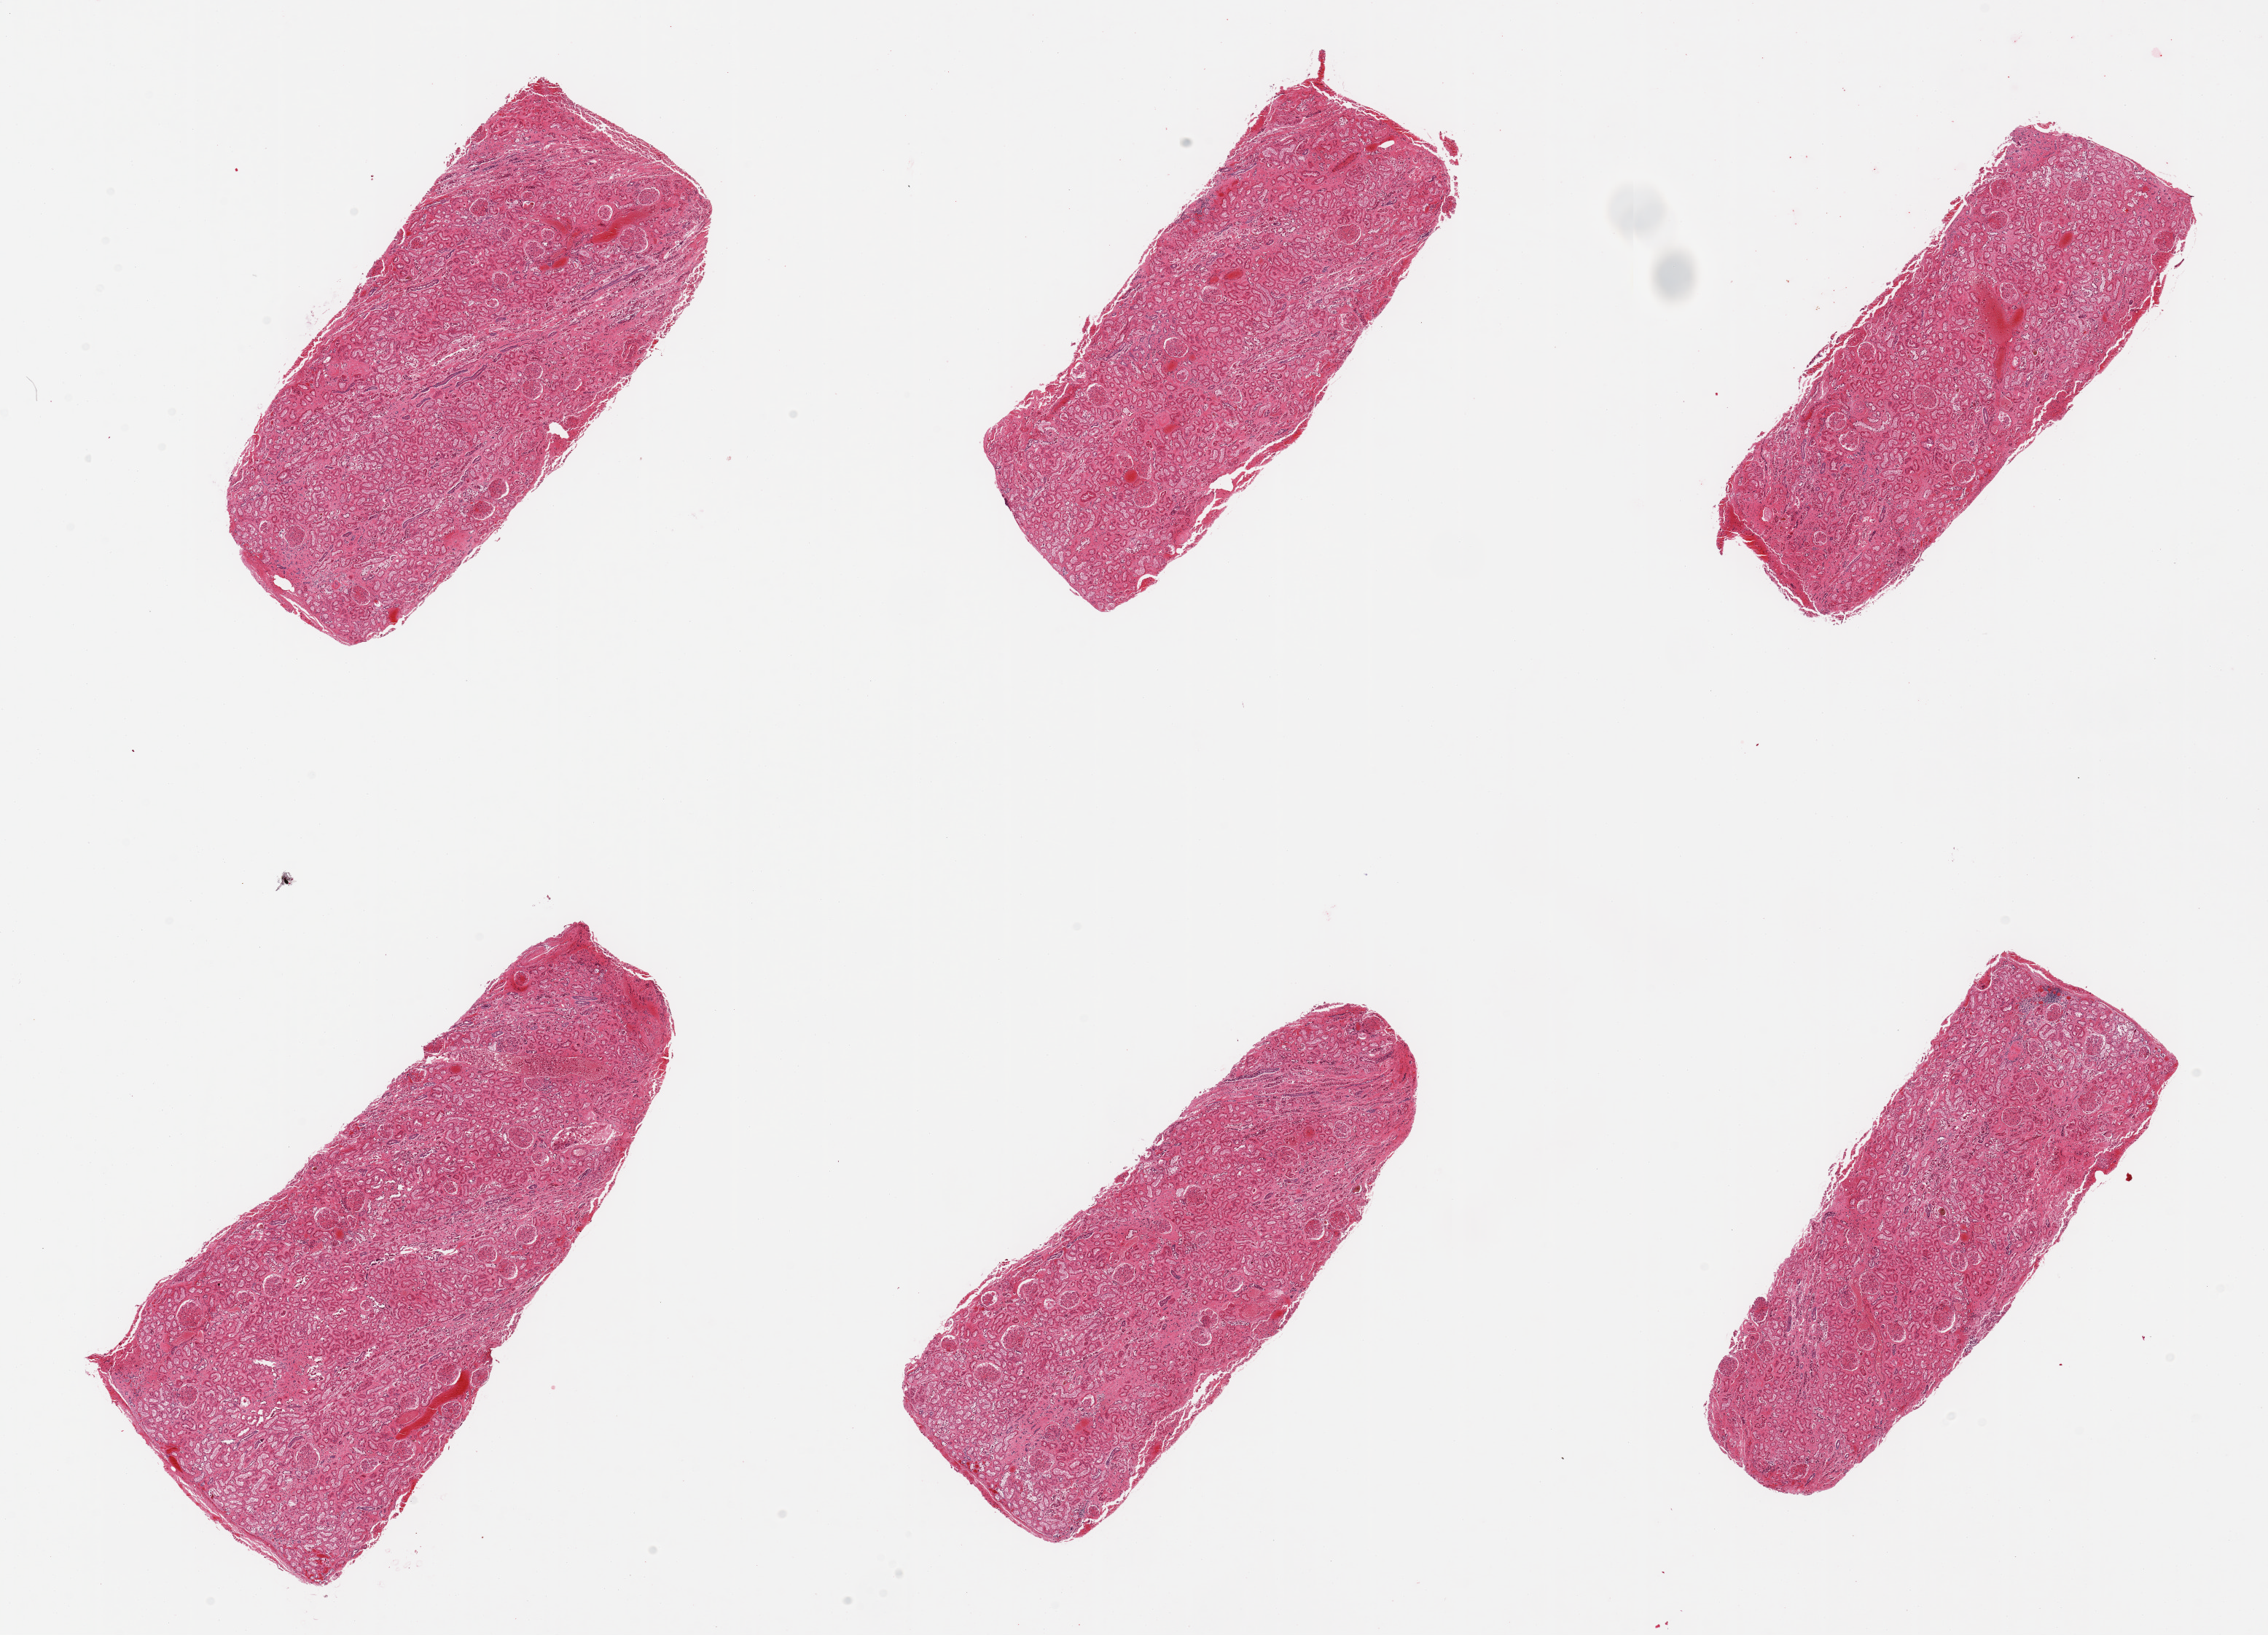
Digitized H&E-stained section — low-resolution overview of the scanned area, about 24.6 x 17.7 mm; PAXgene-fixed, paraffin-embedded tissue; target tissue: renal cortex; tissue donor sample.
• pathologist's review note for this sample: 6 pieces; moderate congestion